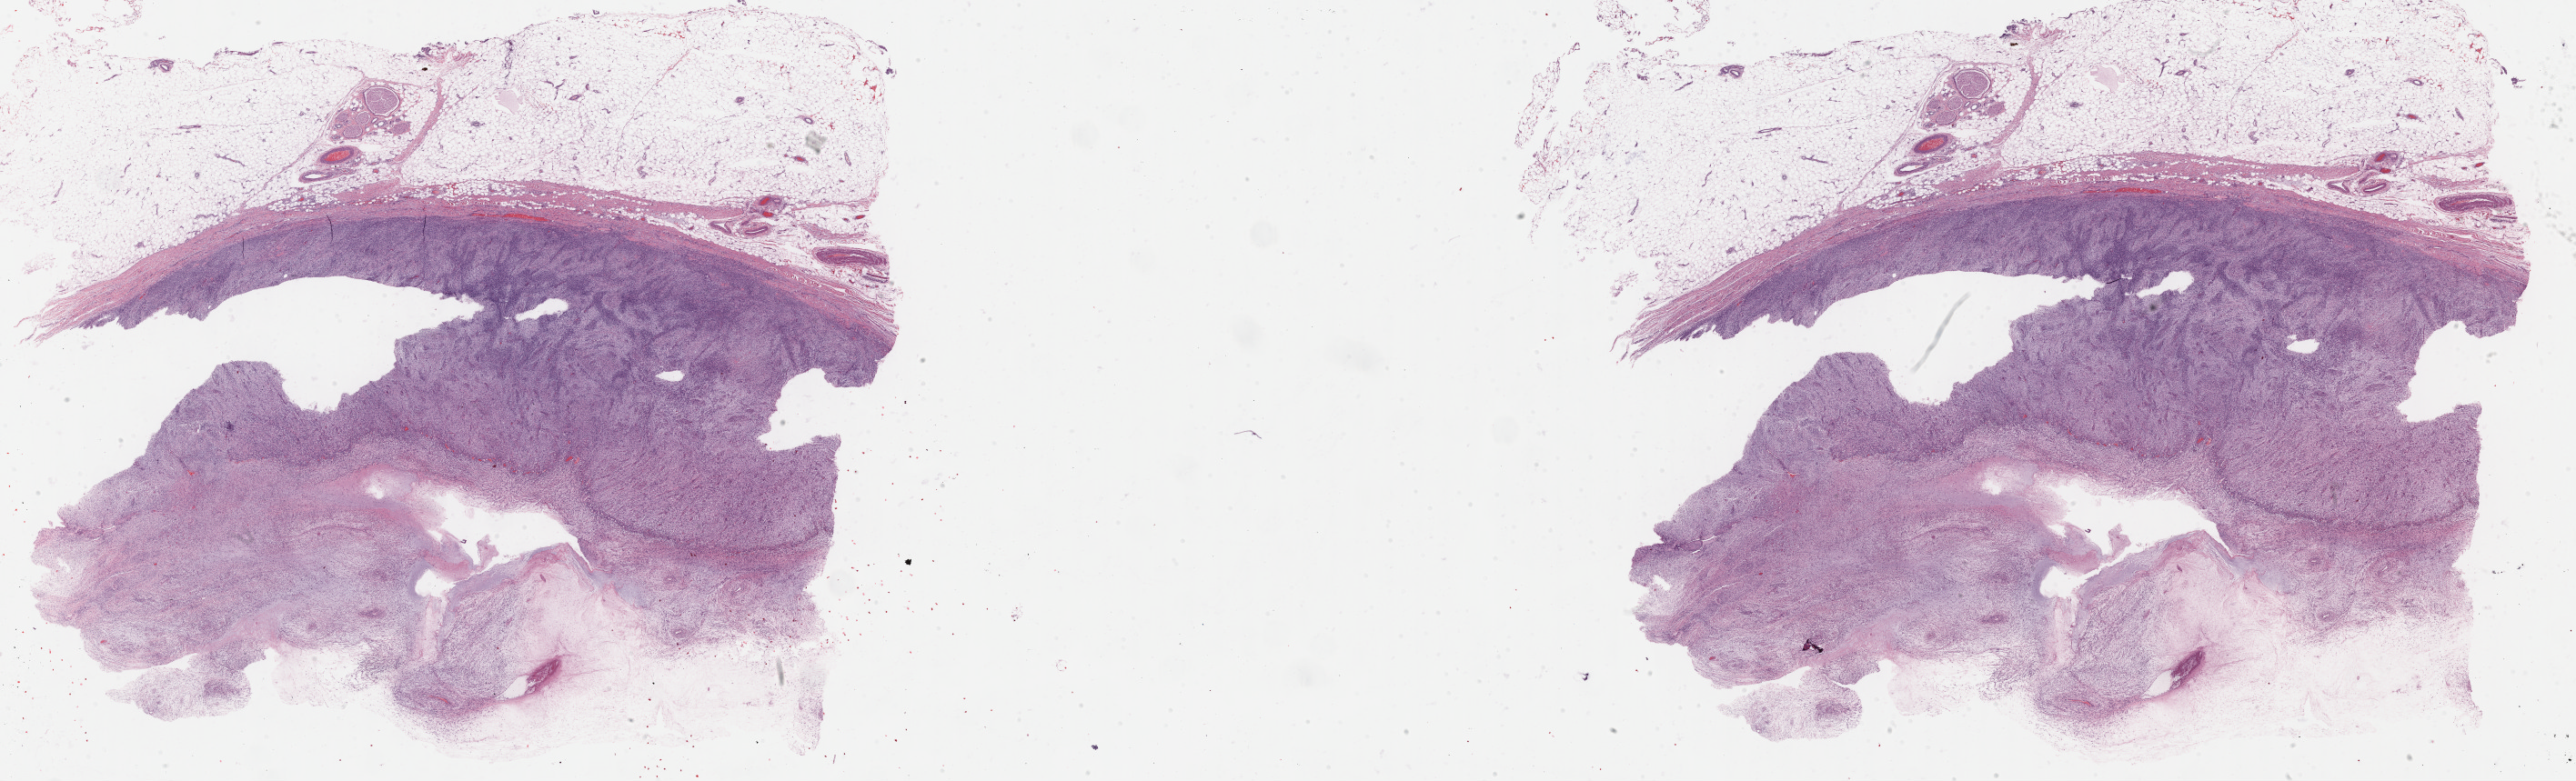
Digitized H&E-stained tissue section (whole slide) — shown as a low-resolution overview of the whole scanned area (about 45.8 x 13.9 mm, from a 40x scan), formalin-fixed paraffin-embedded (FFPE) diagnostic section, sample: primary tumour, connective, subcutaneous and other soft tissues. Patient: female, age at initial diagnosis 53 years.
• diagnosis: Fibromyxosarcoma